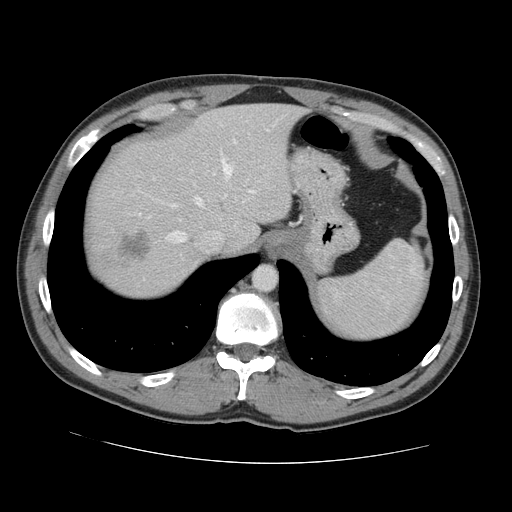
Contrast-enhanced abdominal CT, one axial slice. Slice 112 of 131 in the series (ordered by position). Intravenous contrast given. Soft-tissue window (W 400 / L 40 HU). 512 × 512 image matrix, field of view 380 × 380 mm. Male patient, age 40 years. From the clinical record (not read from this slice): diagnosis: colorectal cancer liver metastases, imaged before liver resection; multiple liver metastases: yes; largest metastasis: 2.9 cm; chemotherapy before resection: yes.
Outlined on this slice (expert manual segmentation):
- hepatic veins: bounding box [x1, y1, x2, y2] px = [166, 159, 232, 243]
- liver: [86, 104, 301, 295]
- planned liver remnant (the part of the liver to remain after resection): [107, 105, 302, 252]
- portal vein (with intrahepatic branches): [214, 140, 255, 193]
- liver metastasis: [115, 231, 150, 264]